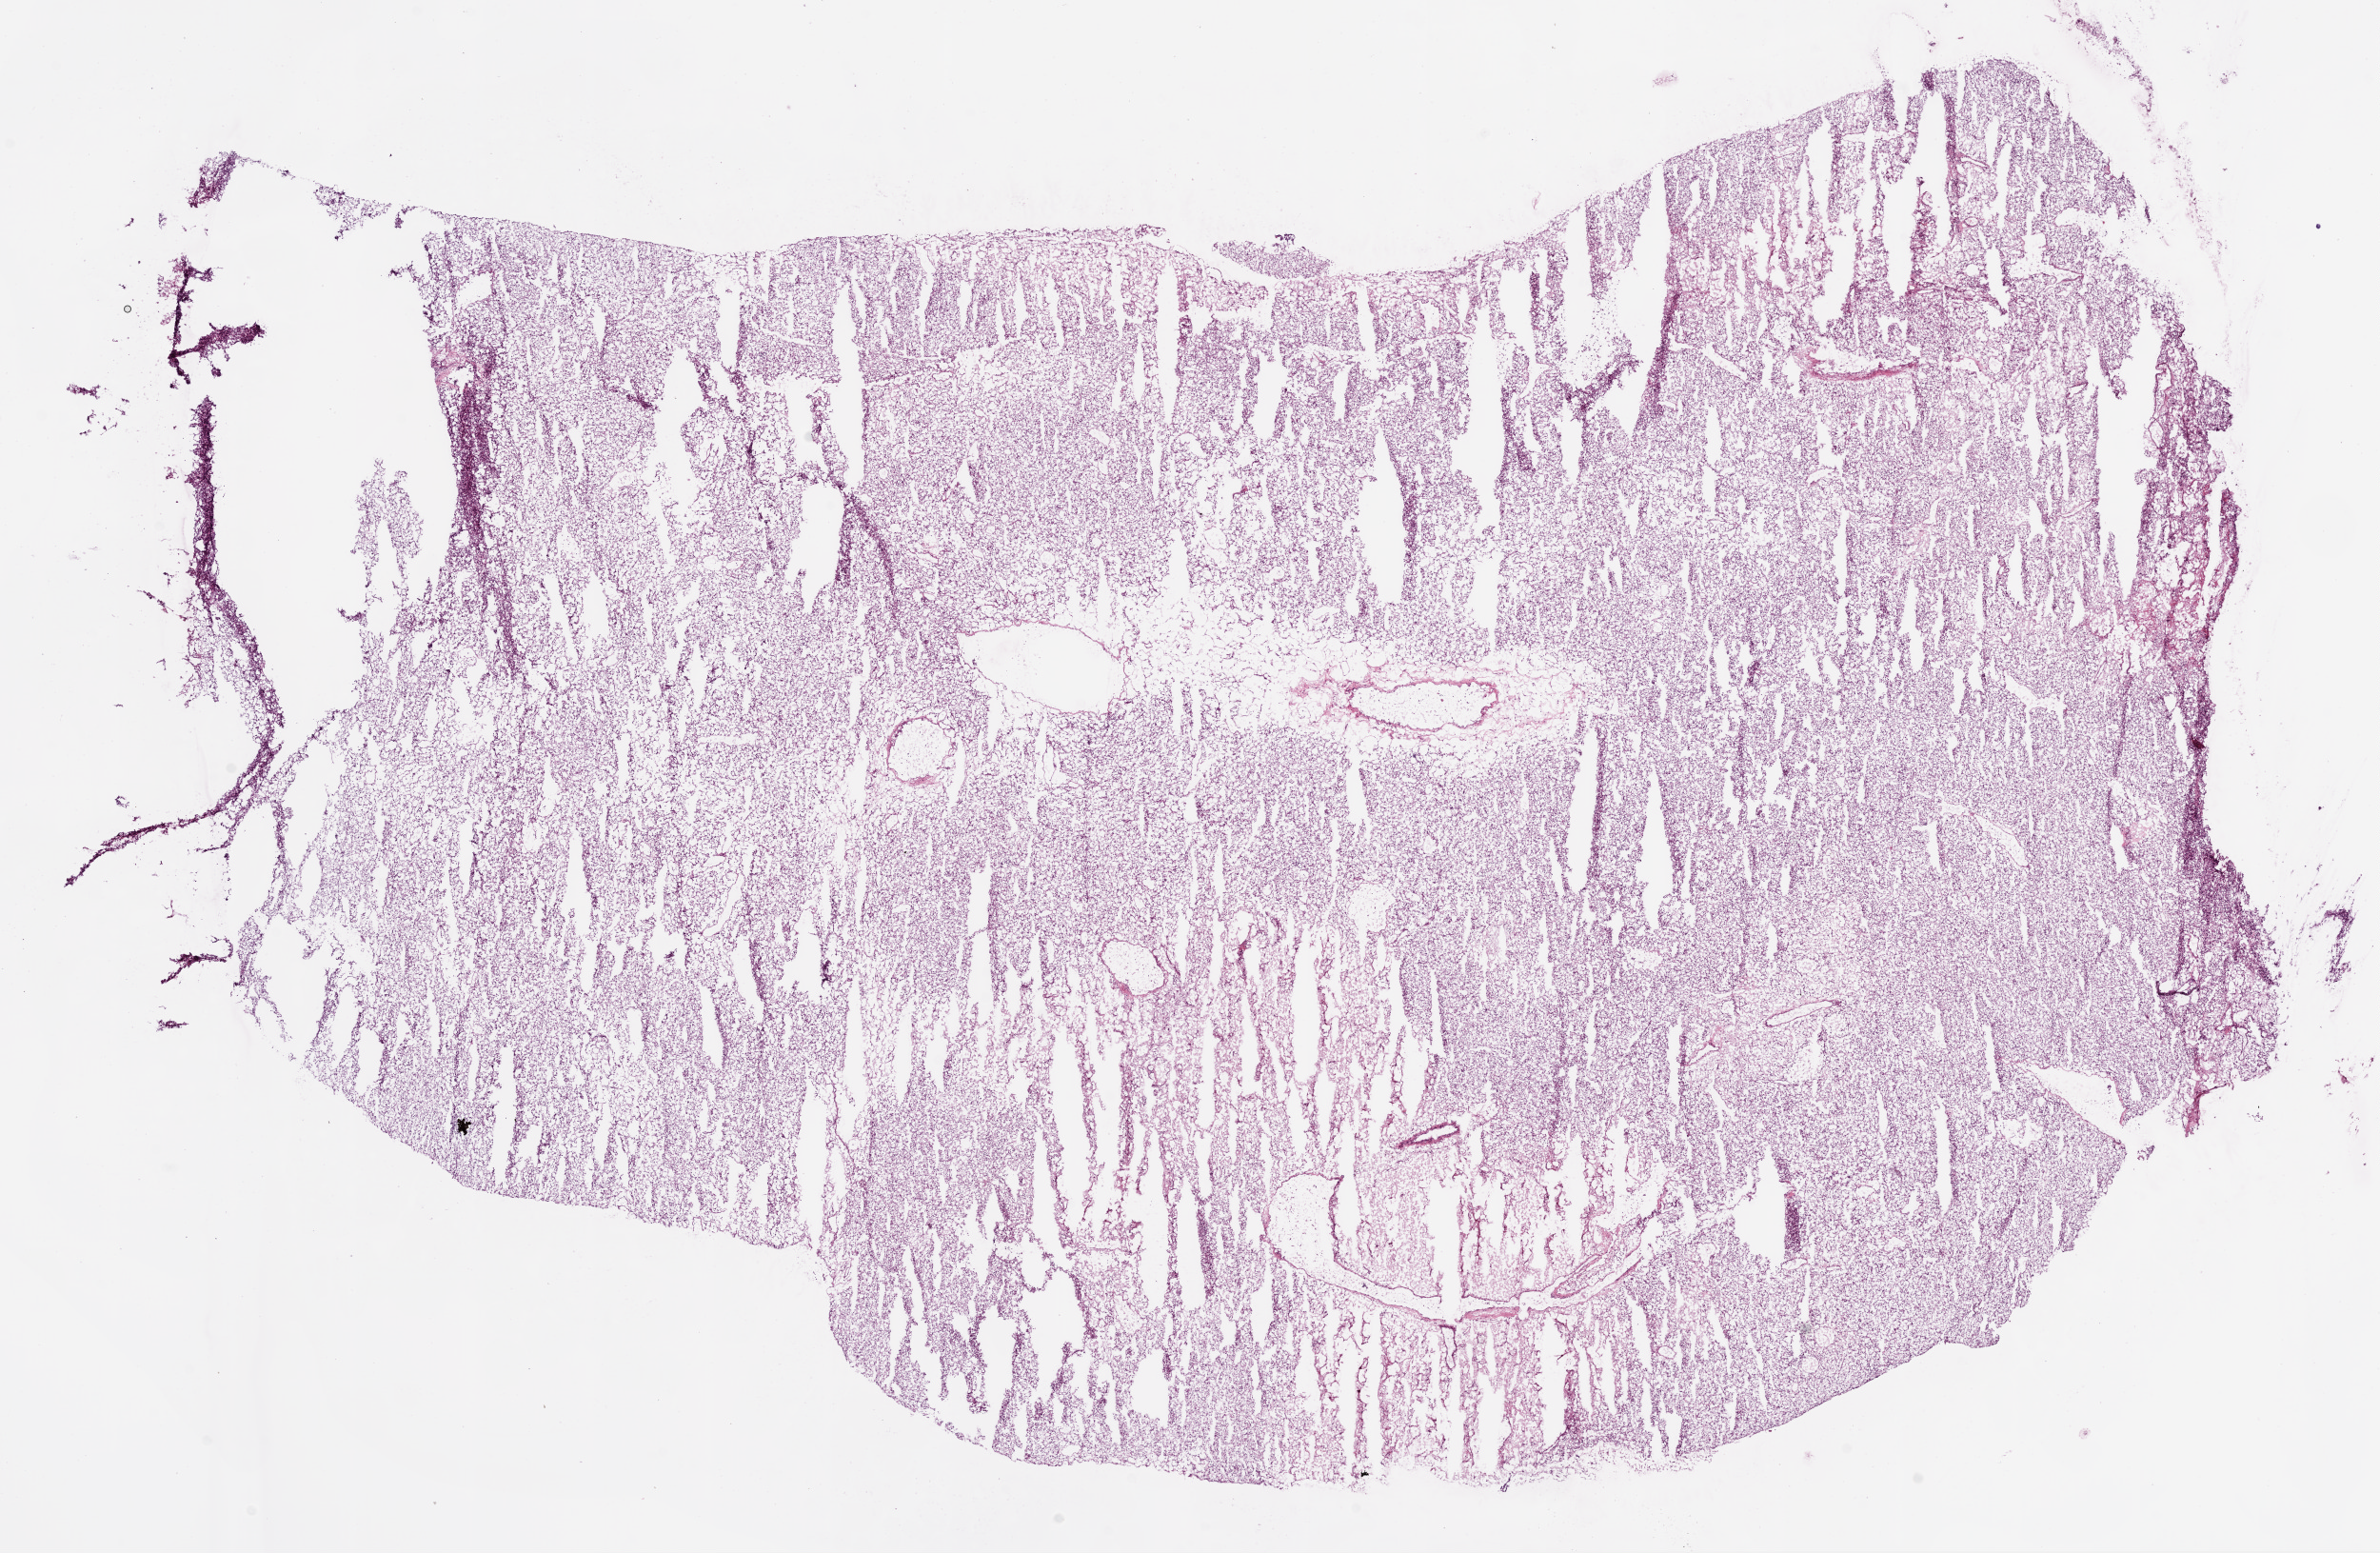
Hematoxylin and eosin (H&E) stained whole-slide image — shown as a low-resolution overview of the whole scanned area (about 20.1 x 13.1 mm, slide scanned at 20x); frozen section from the bottom of the tissue portion; sample: primary tumour, kidney. Female patient; age at initial diagnosis 57 years. Histologic grade: G2 (moderately differentiated). Slide review estimates, as recorded: tumour cells 100%, tumour nuclei 95%, necrosis 0%. Infiltration values recorded for this section: lymphocyte infiltration 1%.
Laterality: right. Histologic diagnosis: Clear cell adenocarcinoma, NOS. TNM: T1a NX M0. AJCC pathologic stage: I.